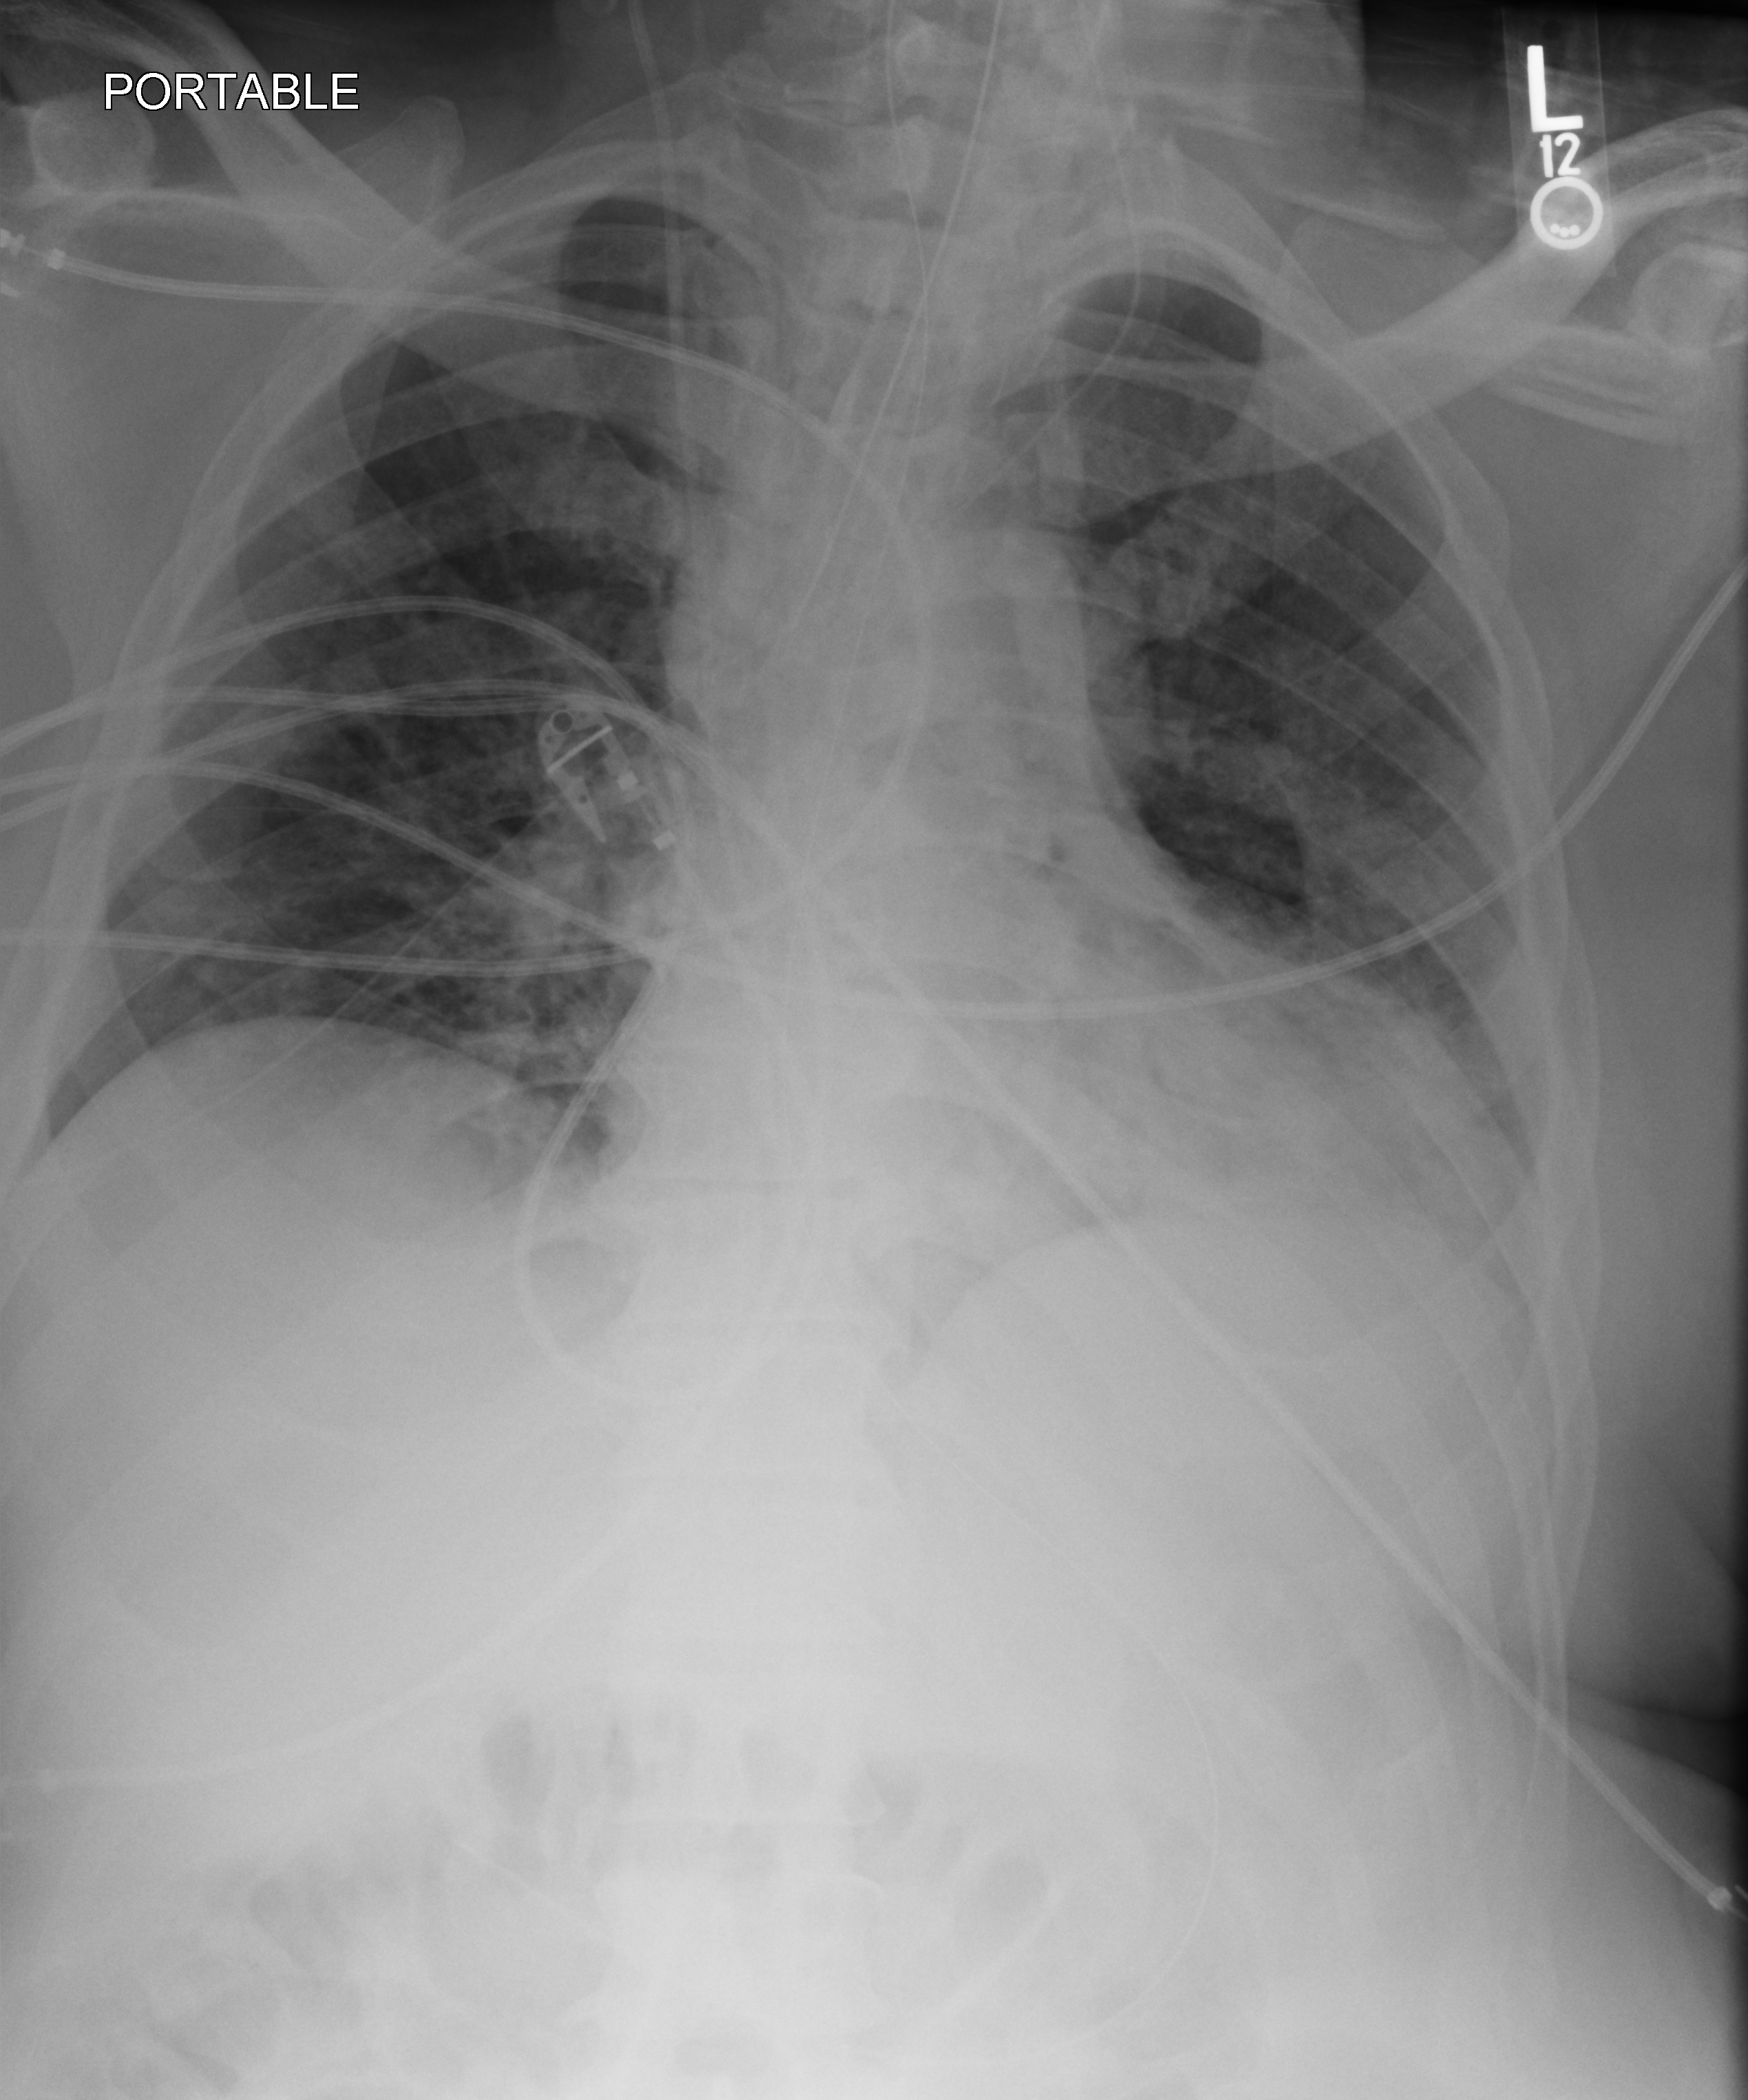
Chest X-ray (portable); anteroposterior (AP) projection. Patient hospitalised with COVID-19; male, aged 18–59 years.
Admission-level facts for this patient (not findings on this image; timing relative to this image not recorded): other chronic lung disease (admission record): no; chronic kidney disease (admission record): no; admitted to intensive care during this hospital stay: yes.